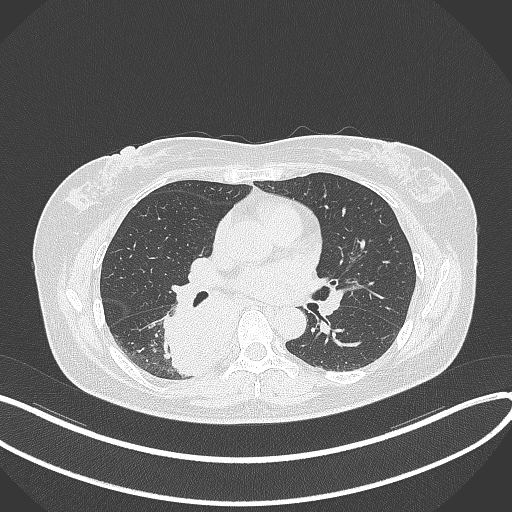
Chest CT, one axial slice; position 191 of 331 along the scan axis; 120 kVp; lung window (W 1500 / L -600 HU); 512 × 512 image matrix, field of view 400 × 400 mm. Patient: female, 54 years. From the clinical record (not read from this slice): clinical TNM (as recorded): T4 N0 M0.
Annotated regions visible in this slice (rectangle marked by the reading radiologist):
- lung tumour (recorded histology: adenocarcinoma): bounding box (x1, y1, x2, y2) in pixels: (156, 293, 244, 382)